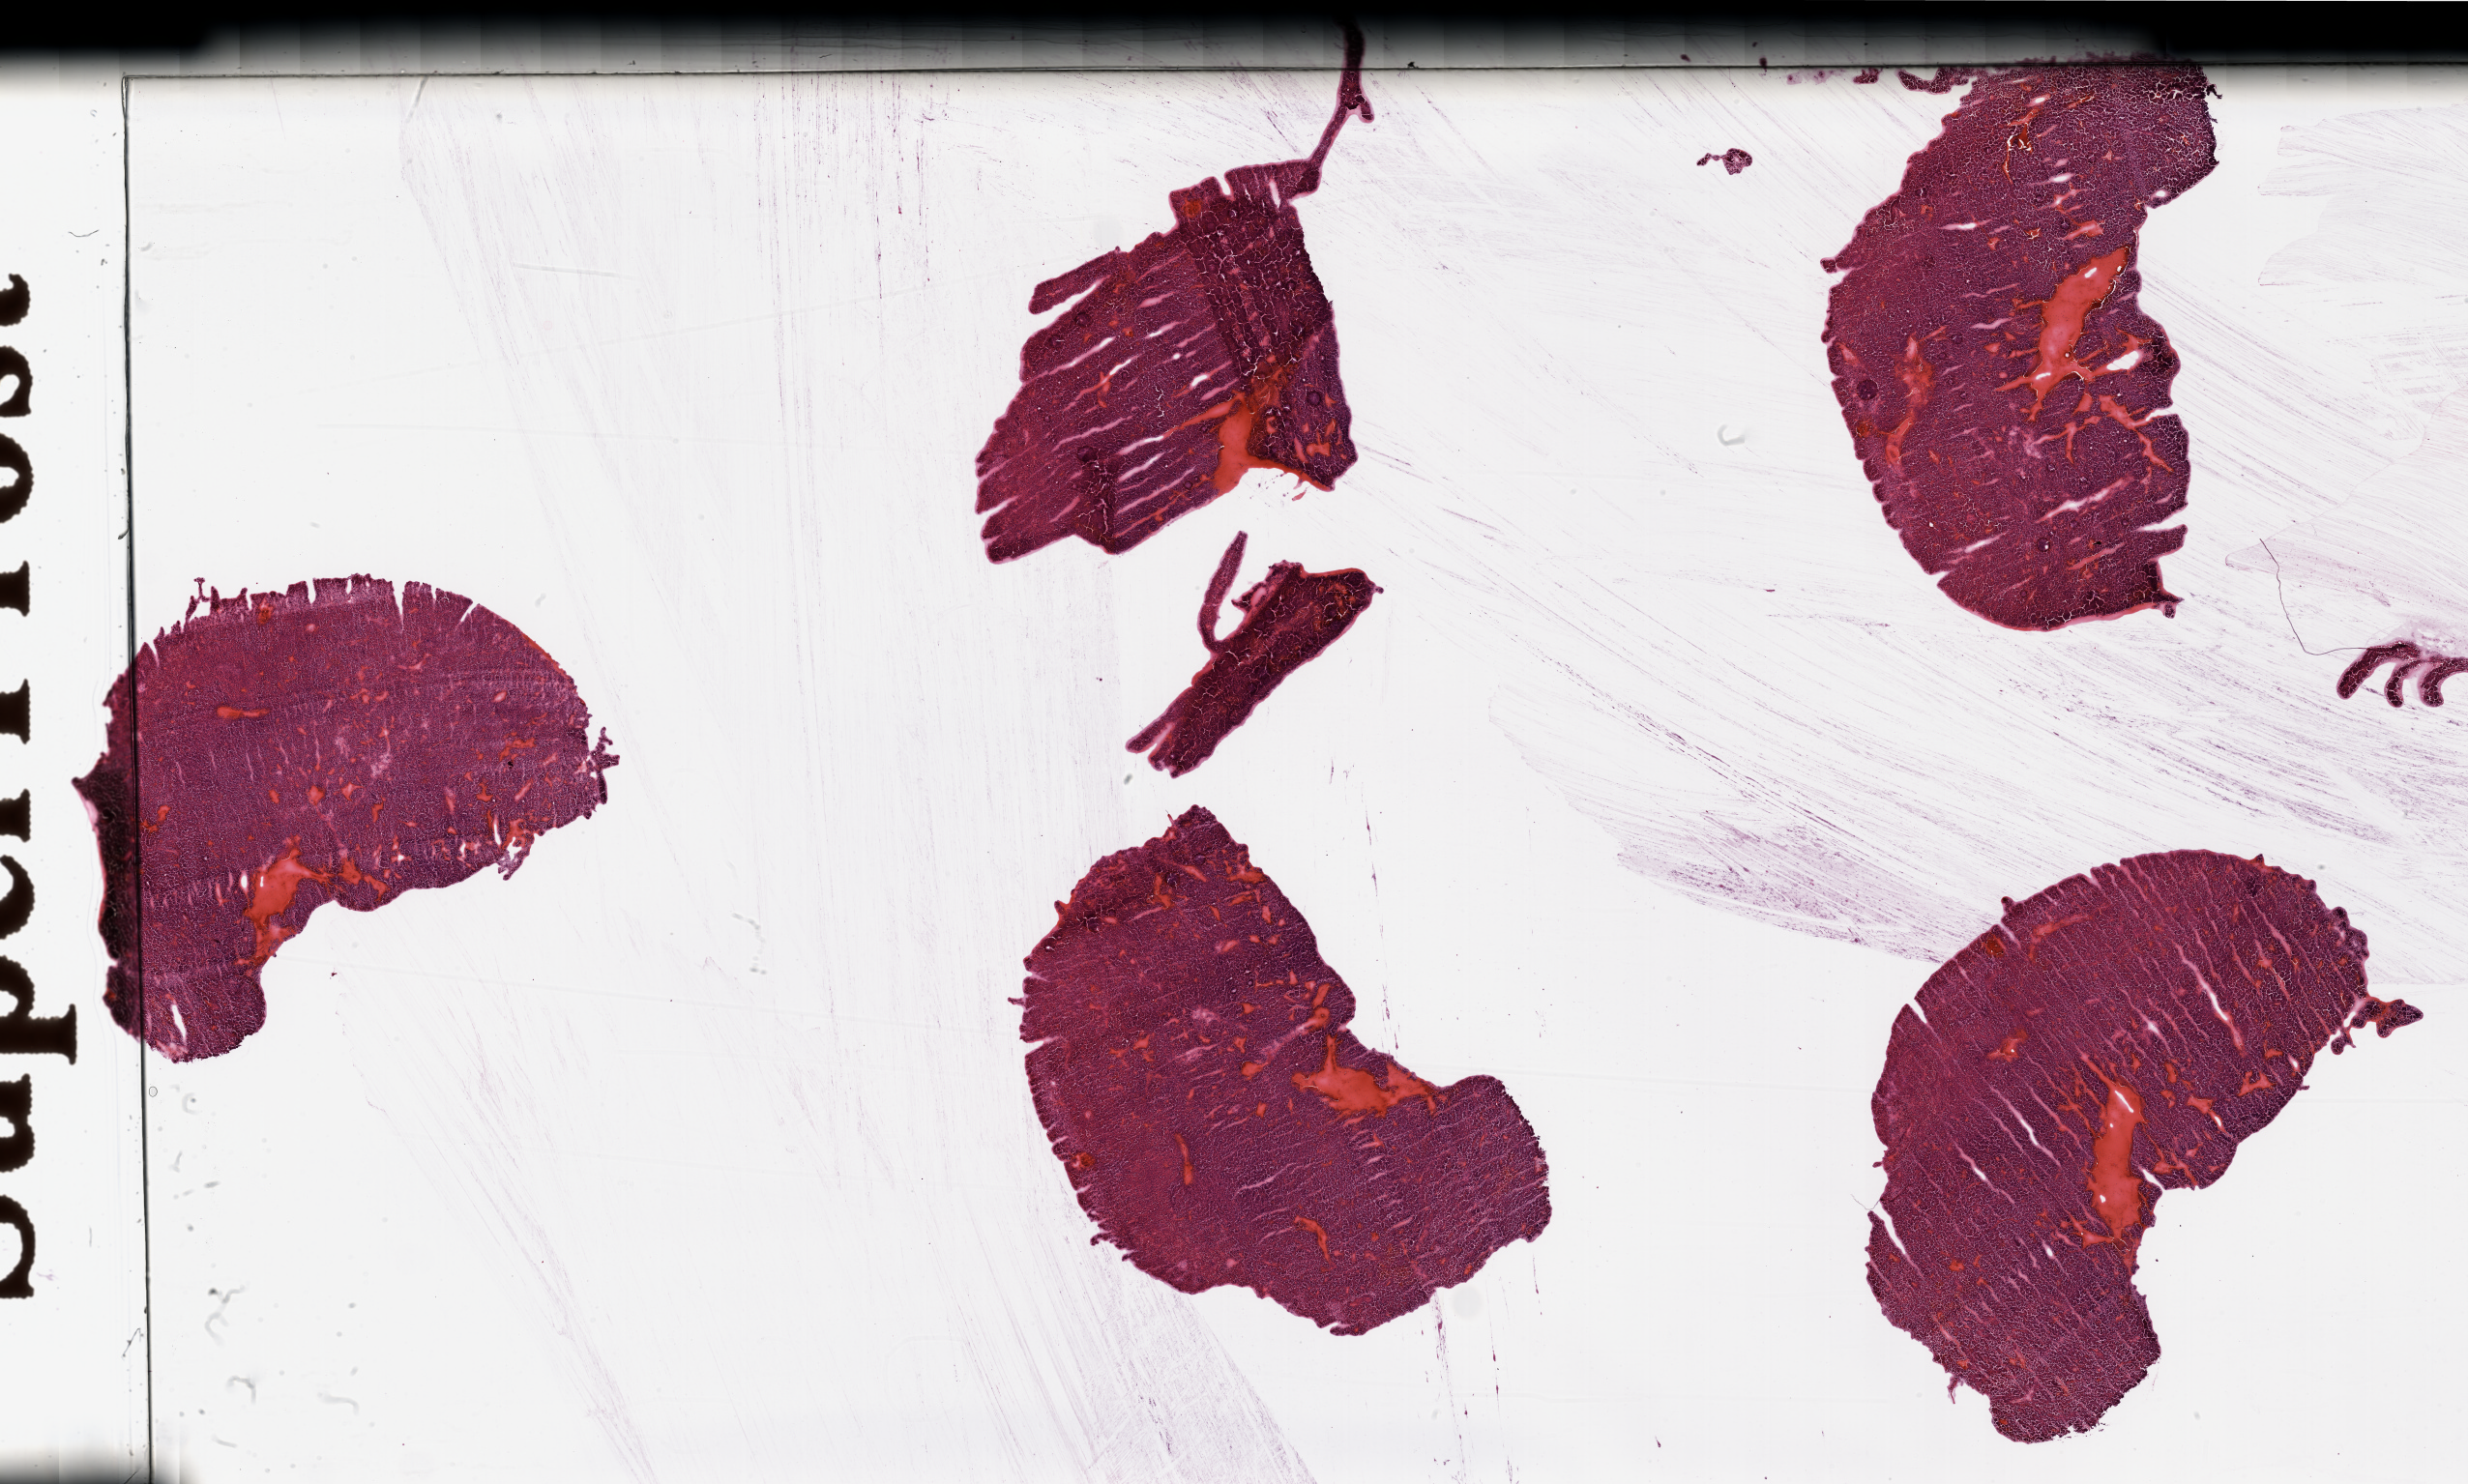
Whole-slide histology image, Hematoxylin and eosin (H&E) stained, shown as a low-resolution overview of the whole scanned area (about 40.4 x 24.3 mm, acquisition: 20x scan); tumour tissue sample, sampled site: kidney. 68-year-old male patient. Histologic grade: G3 (poorly differentiated). Composition of this section per pathologist review: tumour nuclei 90%, necrosis 0%.
Histologic diagnosis: Renal cell carcinoma, NOS. Primary tumour site (as recorded): lower pole. AJCC pathologic stage: III.